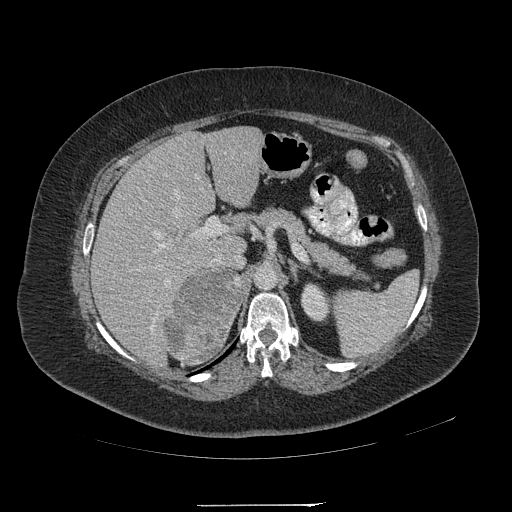
Contrast-enhanced abdominal CT, one axial slice; position 137 of 217 along the scan axis; reconstruction kernel STANDARD; 120 kVp; intravenous contrast given; soft-tissue window (W 400 / L 40 HU); 1.25 mm slice thickness; 512 × 512 image matrix. Female patient, age 55 years. Case-level facts recorded for this patient, not image findings: diagnosis: adrenocortical carcinoma; tumour side: right adrenal; tumour size at pathology: 11 cm; Ki-67 index: 20 %; stage (as recorded): 2.
Structures marked on this image (semi-automatically segmented with operator editing):
- mass: bounding box (x1, y1, x2, y2) in pixels: (165, 271, 240, 360)